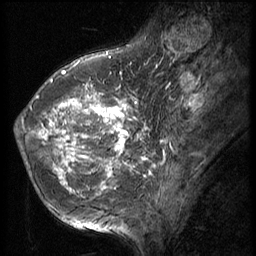
Breast MRI (dynamic contrast-enhanced), one sagittal slice. Slice 20 of 56 in the series (ordered by position). 3 images stored at this slice position (order not interpretable as contrast timing). 1.5 T. TE 4.2 ms, TR 9 ms. 2.5 mm slice thickness. 256 × 256 image matrix, field of view 180 × 180 mm. Female patient, age 49 years. Case-level facts recorded for this patient, not image findings: setting: breast cancer imaged before/during neoadjuvant chemotherapy; receptor status: HER2-positive.
Outlined on this slice (semi-automatic segmentation, software-assisted and operator-edited):
- analysis volume of interest (the breast-tissue region the enhancement analysis was run in; not a lesion): bounding box [x1, y1, x2, y2] px = [15, 79, 137, 203]
- tumour enhancement mask (voxels above the 140 % enhancement threshold inside the analysis volume of interest): [16, 86, 136, 192]